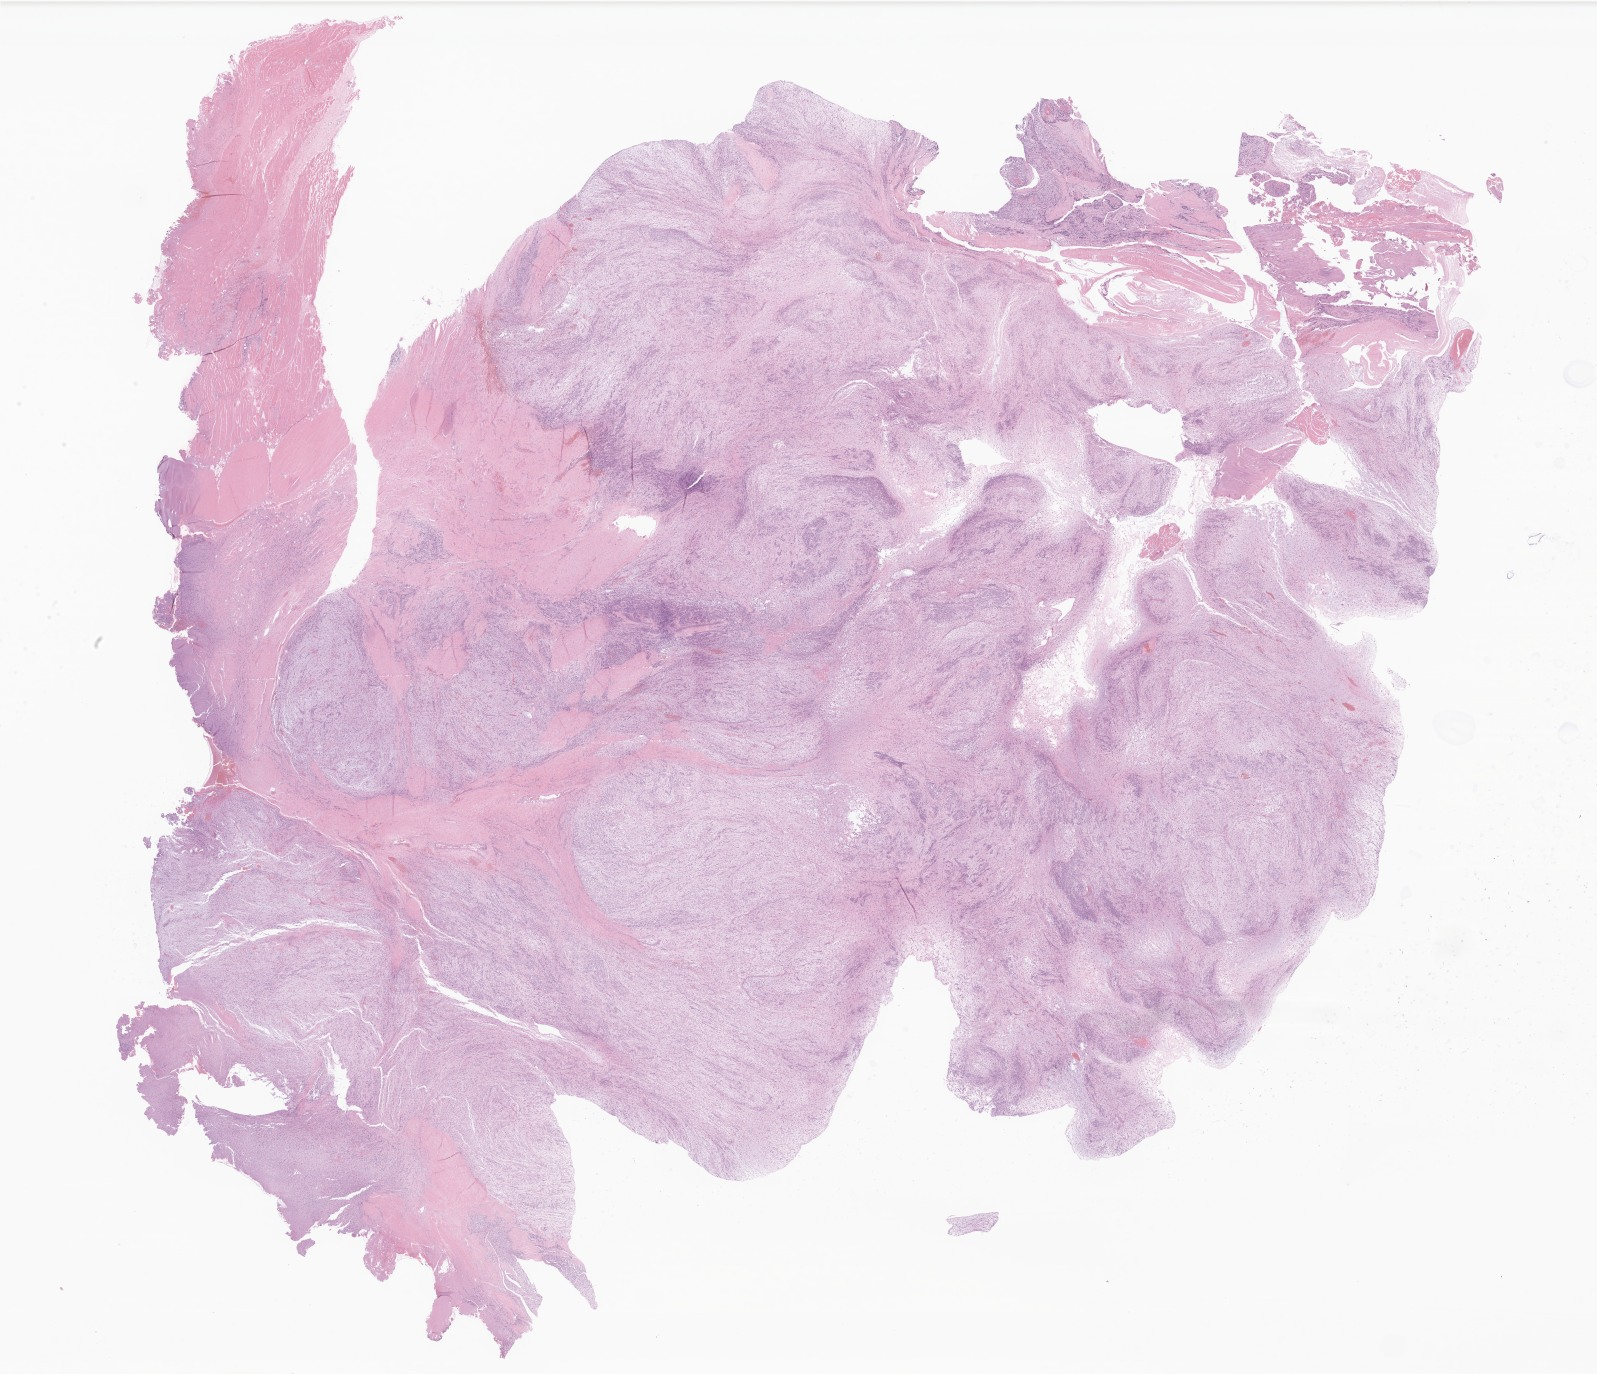
Digitized H&E-stained section of tumor tissue from the soft tissue of trunk — whole scanned area (about 26.9 x 23.2 mm) shown as a low-resolution overview. Formalin-fixed, paraffin-embedded (FFPE) tissue. Patient male; age 60 months.
* recorded diagnosis: Spindle cell rhabdomyosarcoma
* tissue or organ of origin (case record): connective, subcutaneous and other soft tissues of trunk